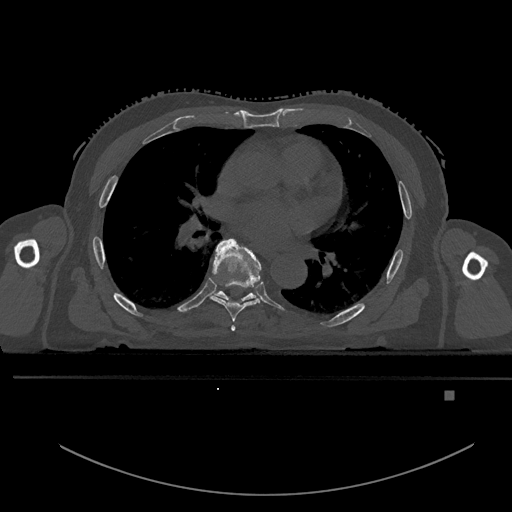
CT including the spine, one axial slice; bone window (W 1800 / L 400 HU); 0.5 mm slice thickness; 512 × 512 image matrix, field of view 456 × 456 mm. Patient: male, 82 years. From the clinical record (not read from this slice): primary cancer: prostate.
Structures marked on this image (semi-automatic segmentation, software-assisted and operator-edited):
- T5 vertebra: bounding box (x1, y1, x2, y2) in pixels: (231, 325, 236, 331)
- T6 vertebra: (210, 238, 261, 322)
- T7 vertebra: (214, 291, 256, 301)